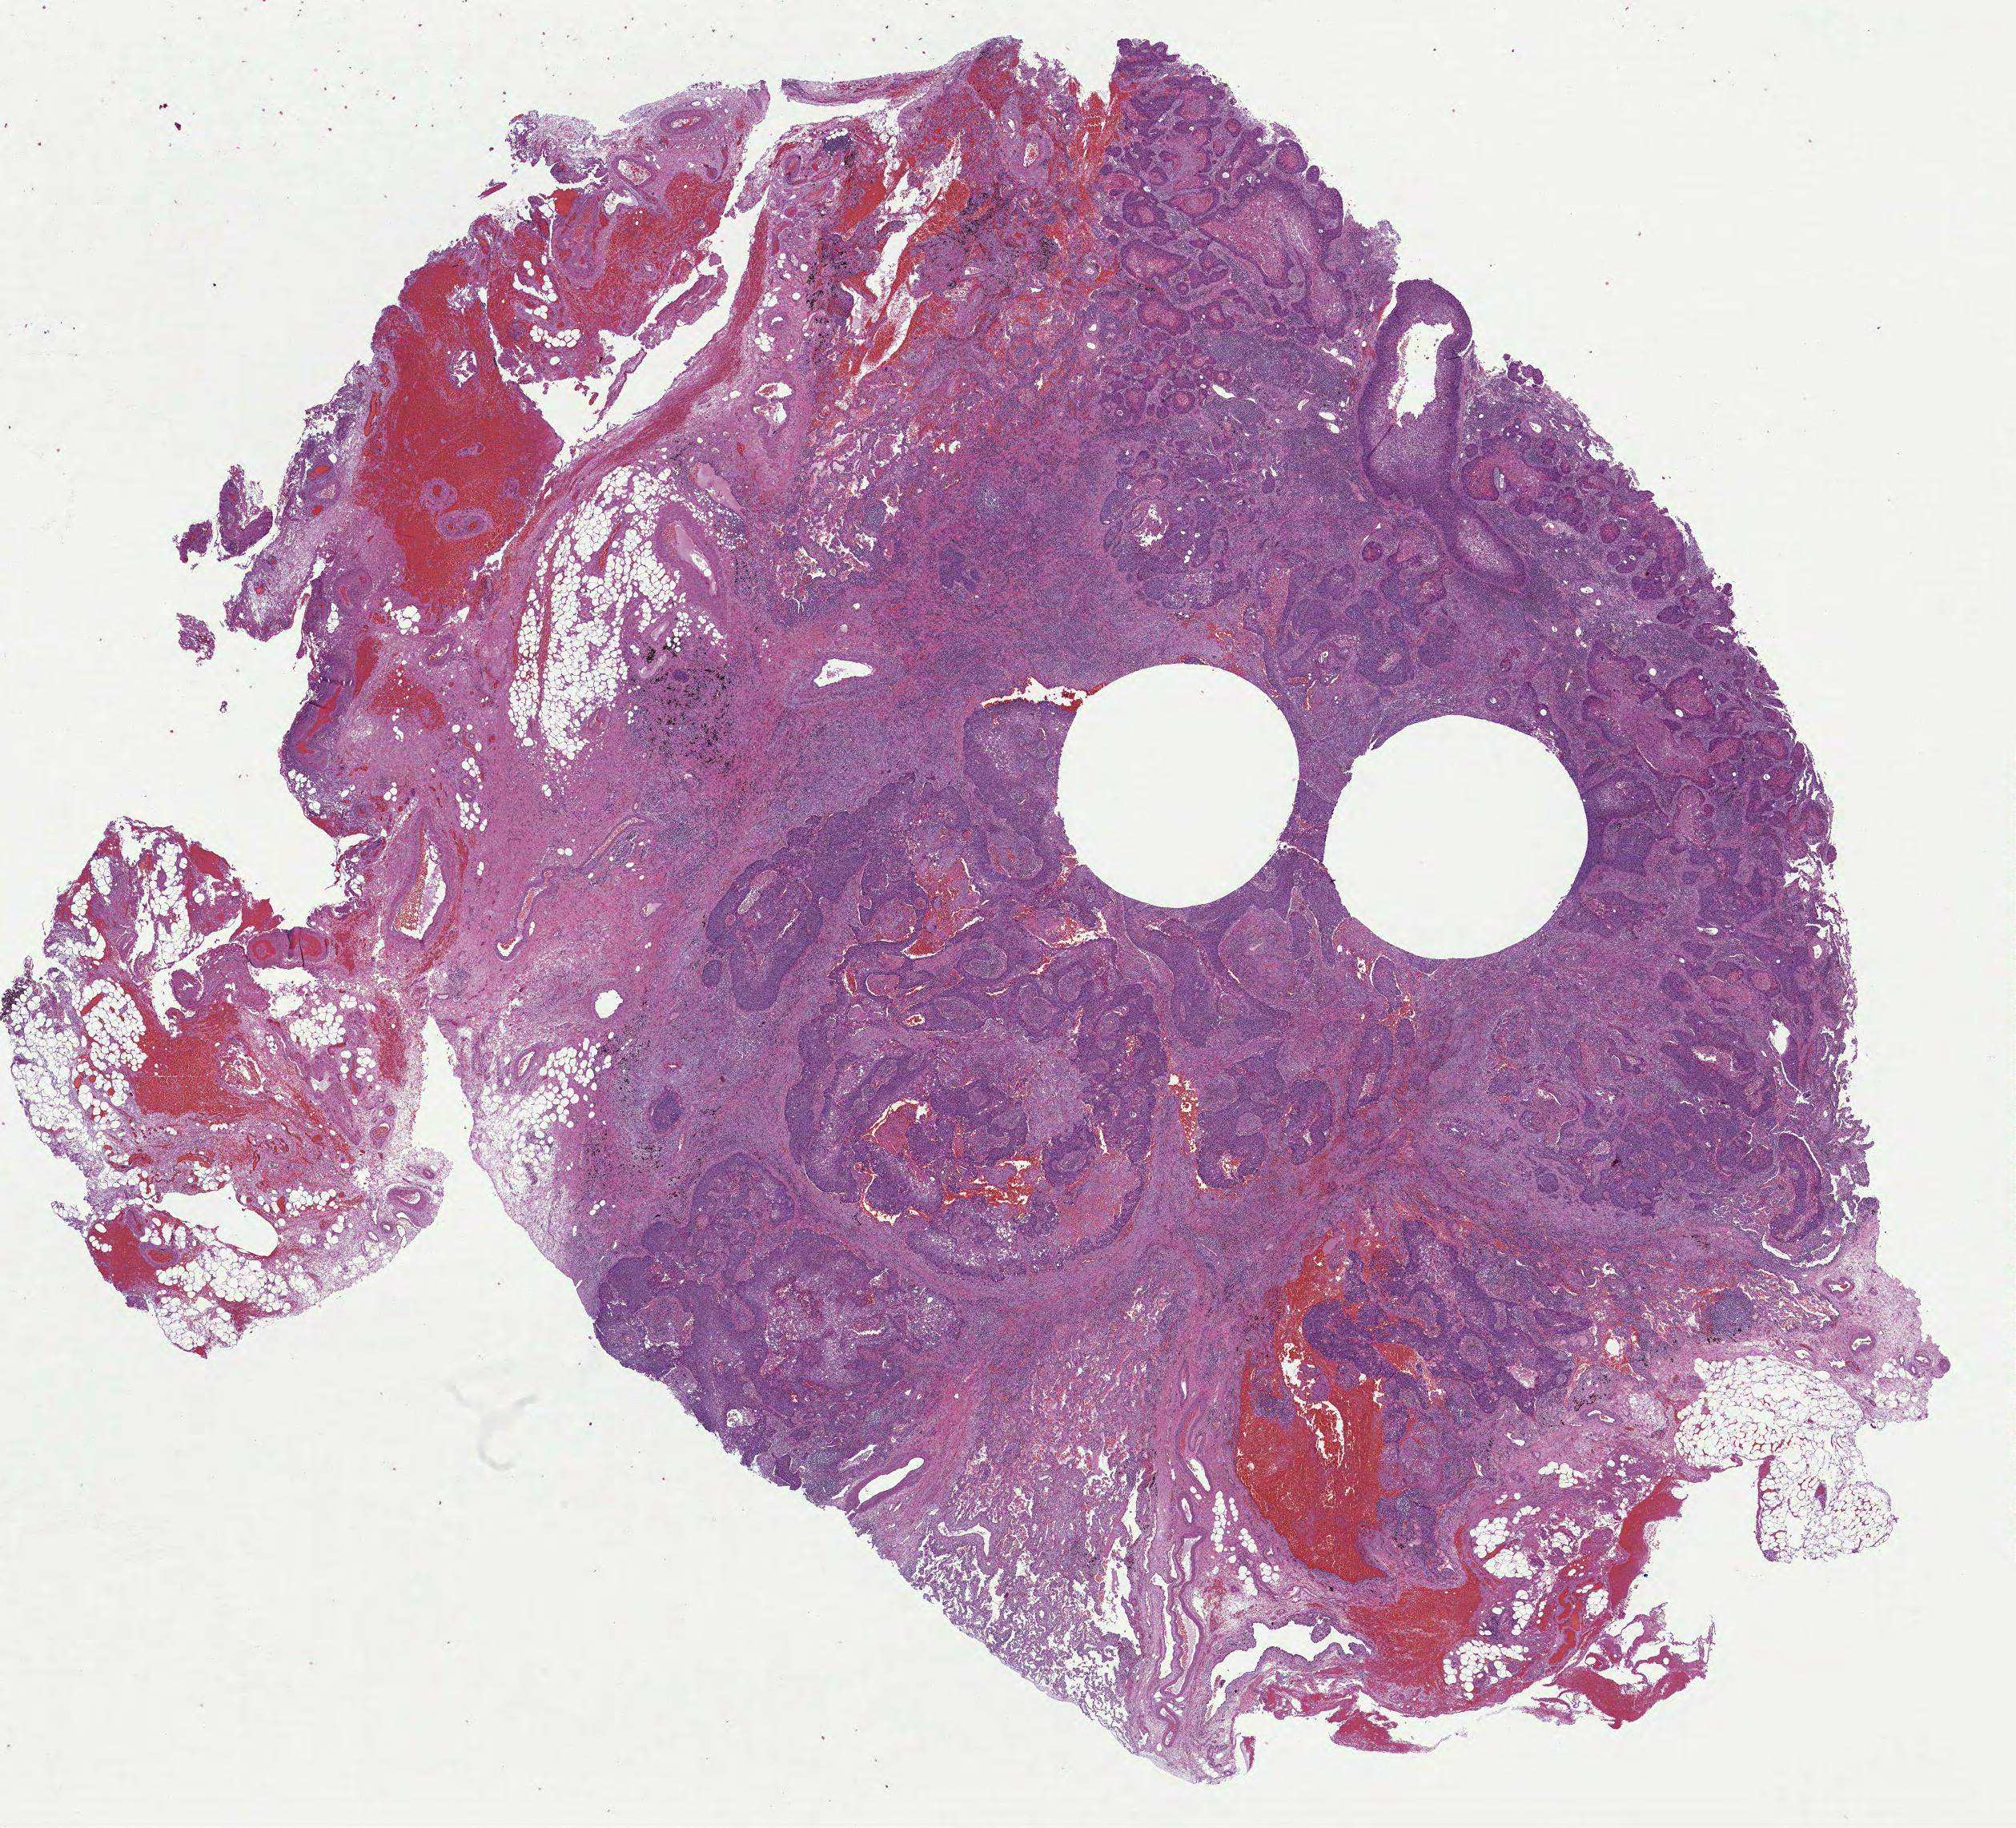
Whole-slide histology image, H&E — low-resolution overview of the scanned area, about 20.3 x 18.4 mm (from a 40x scan); formalin-fixed paraffin-embedded (FFPE) diagnostic section; lung, primary tumour sample. Male patient; age at initial diagnosis 79 years.
Diagnosis: Squamous cell carcinoma, NOS (upper lobe, lung).